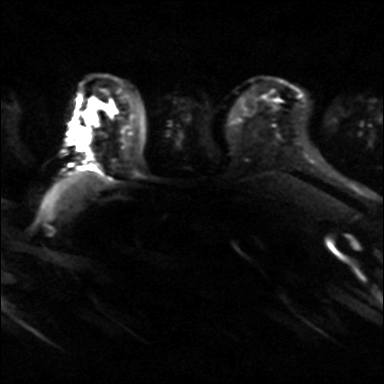
Breast MRI, one axial slice. Slice 26 of 36 in the series (ordered by position). Diffusion-weighted series; image 2 of 4 stored at this slice position (different b-values; order by instance number). 3 T. 4 mm slice thickness. 384 × 384 image matrix. Female patient.
Outlined on this slice (expert manual segmentation):
- tumour on diffusion-weighted imaging: bounding box [x1, y1, x2, y2] px = [82, 115, 99, 139]